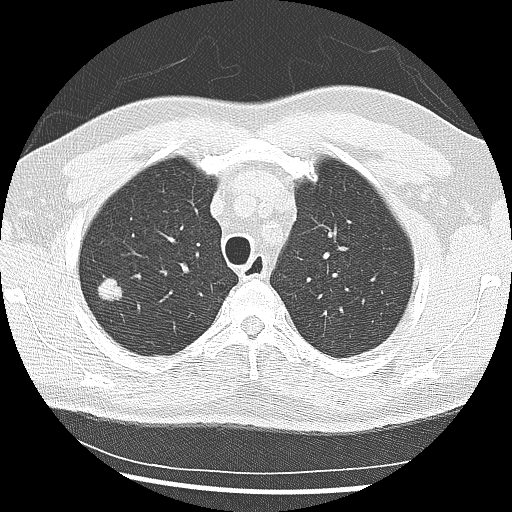
Low-dose screening chest CT, one axial slice; position 208 of 265 along the scan axis; 120 kVp; lung window (W 1500 / L -600 HU); 2.5 mm slice thickness; 512 × 512 image matrix, field of view 340 × 340 mm.
Outlined on this slice (expert manual segmentation):
- lesion 1 (tumor, upper lobe of right lung): bounding box [x1, y1, x2, y2] px = [98, 278, 123, 302]